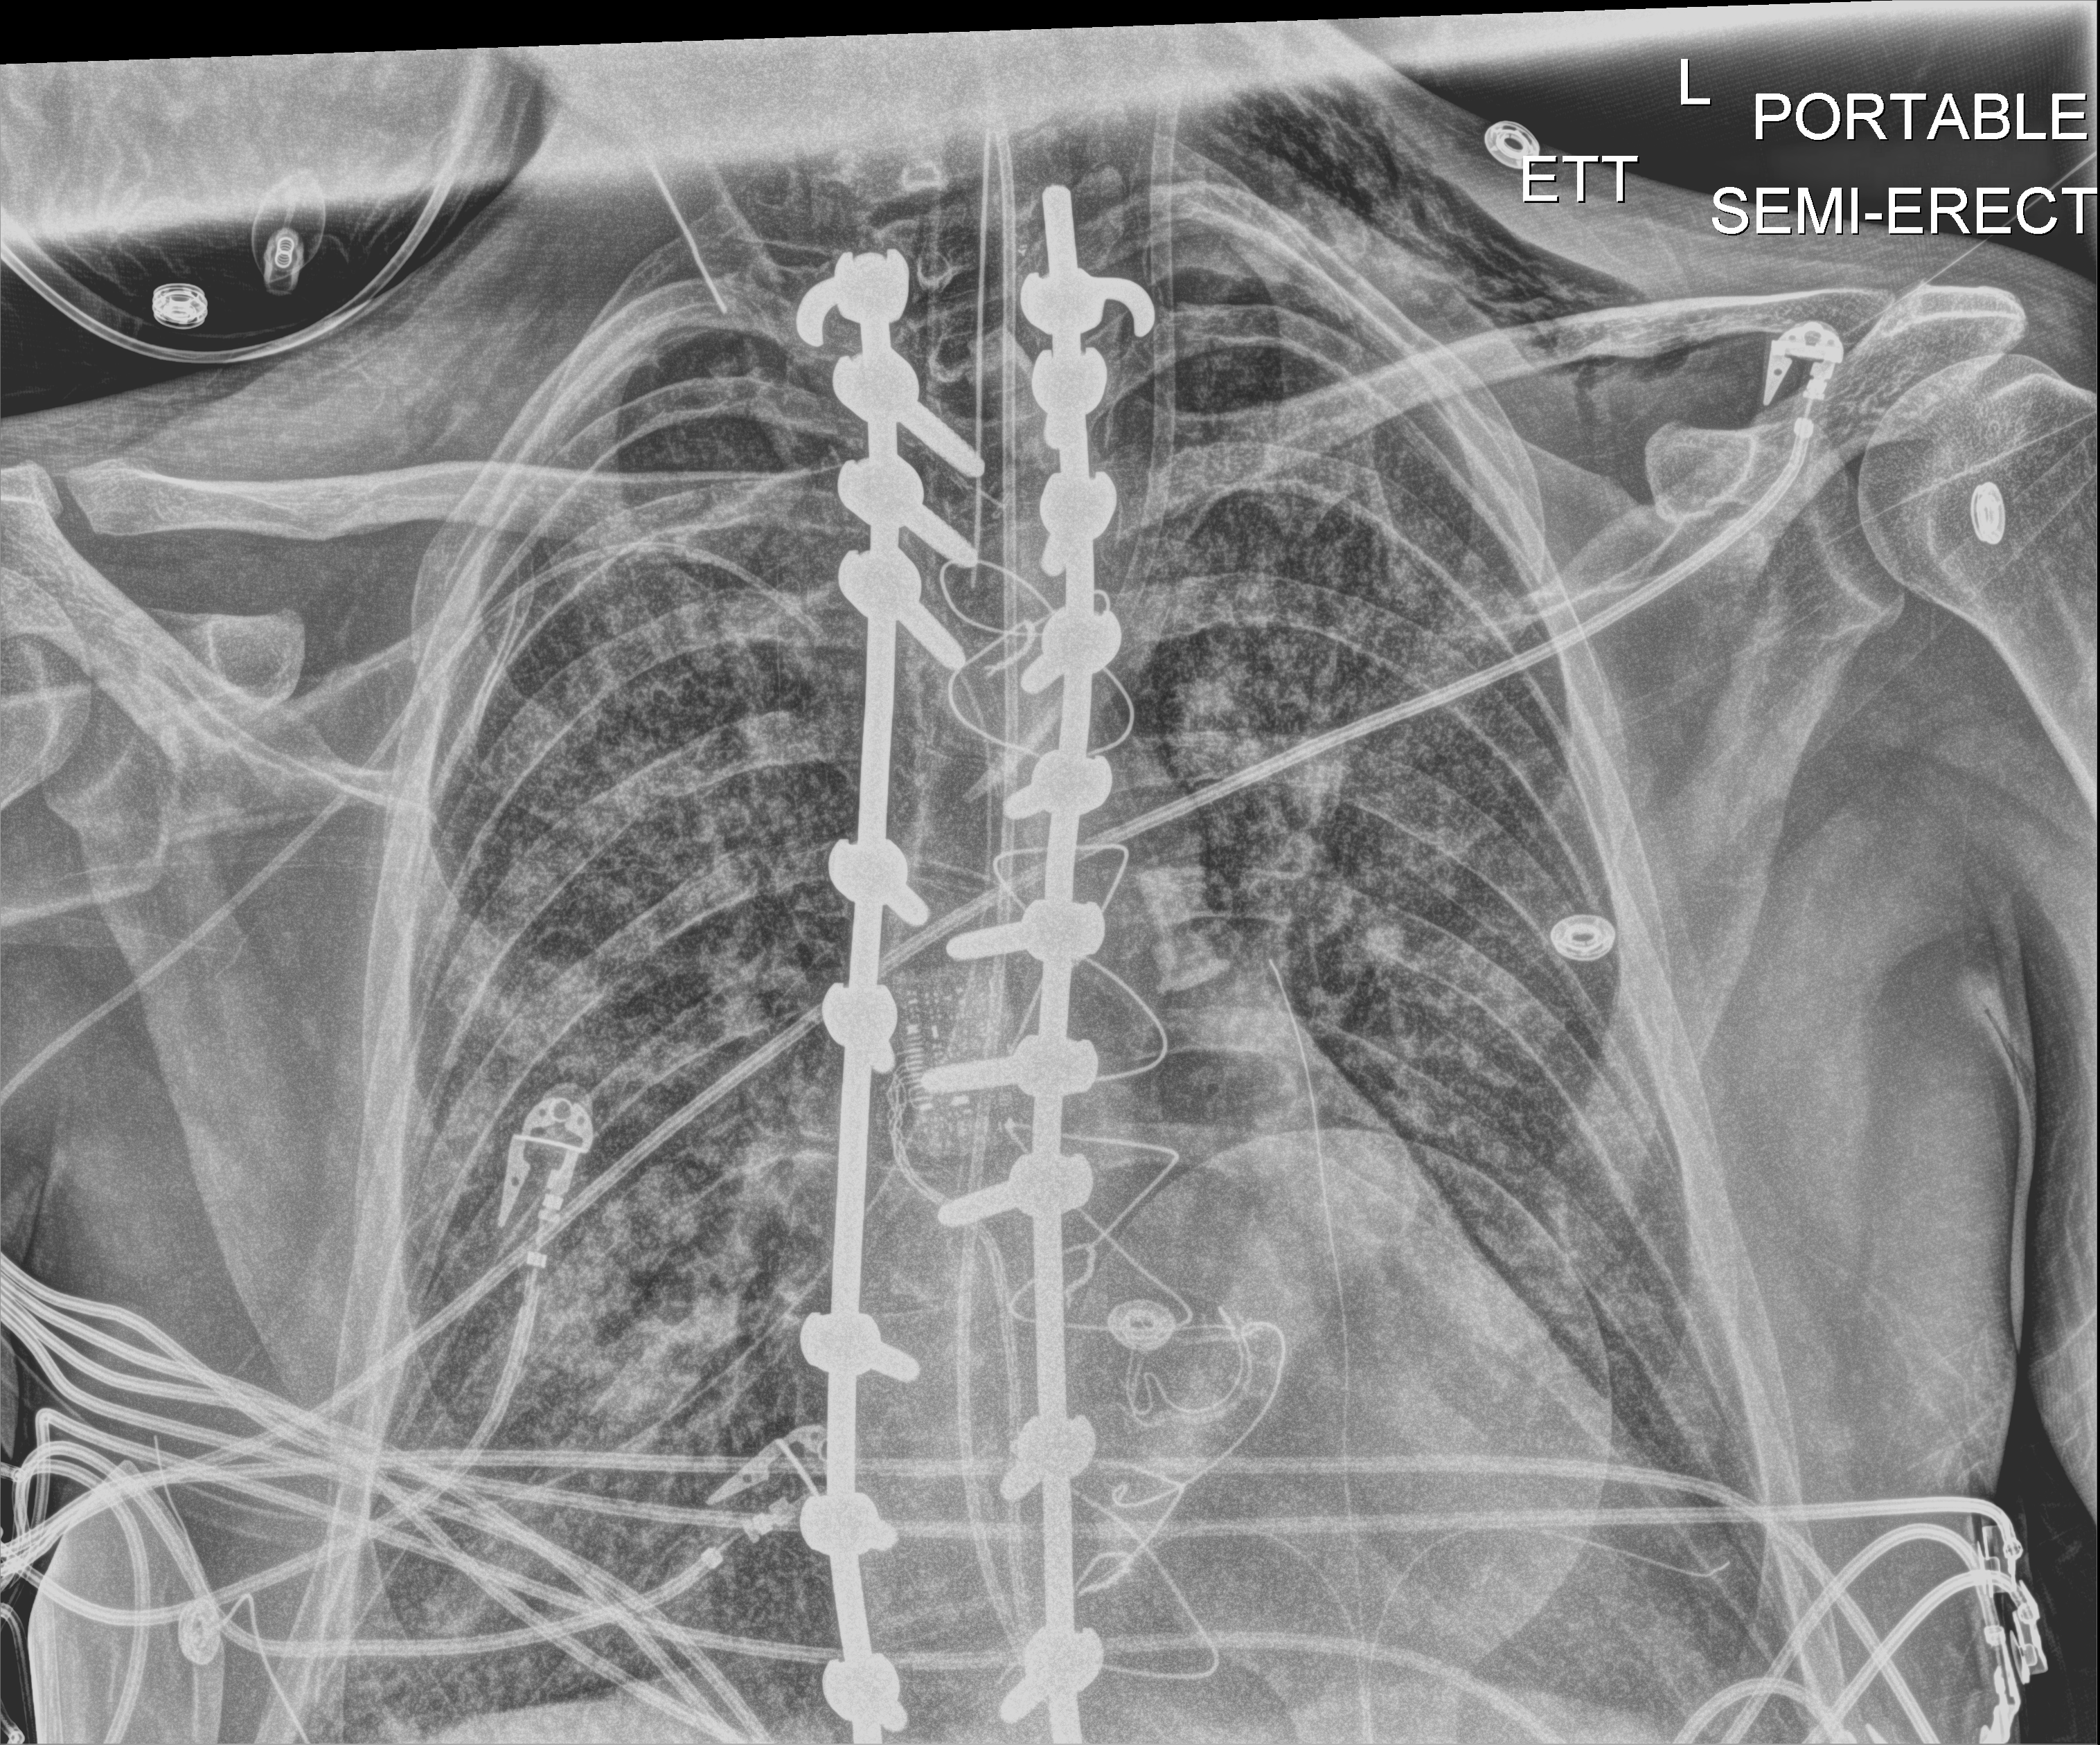
Portable chest radiograph, anteroposterior (AP) projection. Adult patient hospitalised with COVID-19, age 18–59 years.
From the hospital-stay record, not from the radiograph (when in the stay this image was taken is not recorded): mechanically ventilated during this hospital stay: yes.